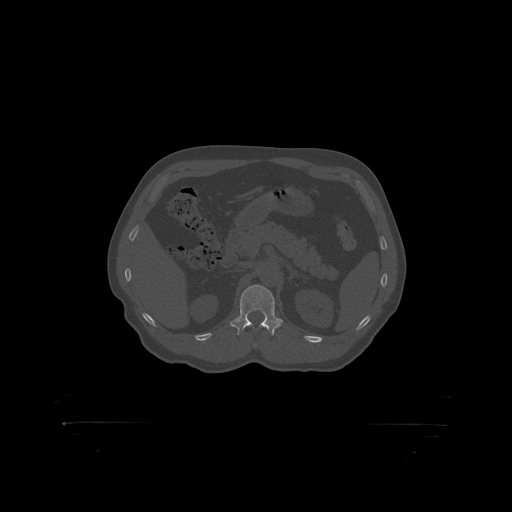
CT including the spine, one axial slice. Position 330 of 399 along the scan axis. Bone window (W 1800 / L 400 HU). 512 × 512 image matrix, field of view 650 × 650 mm. Patient: male, 46 years. Case-level facts recorded for this patient, not image findings: primary cancer: skin.
Outlined on this slice (semi-automatically segmented with operator editing):
- L1 vertebra: bounding box [x1, y1, x2, y2] px = [240, 285, 275, 319]